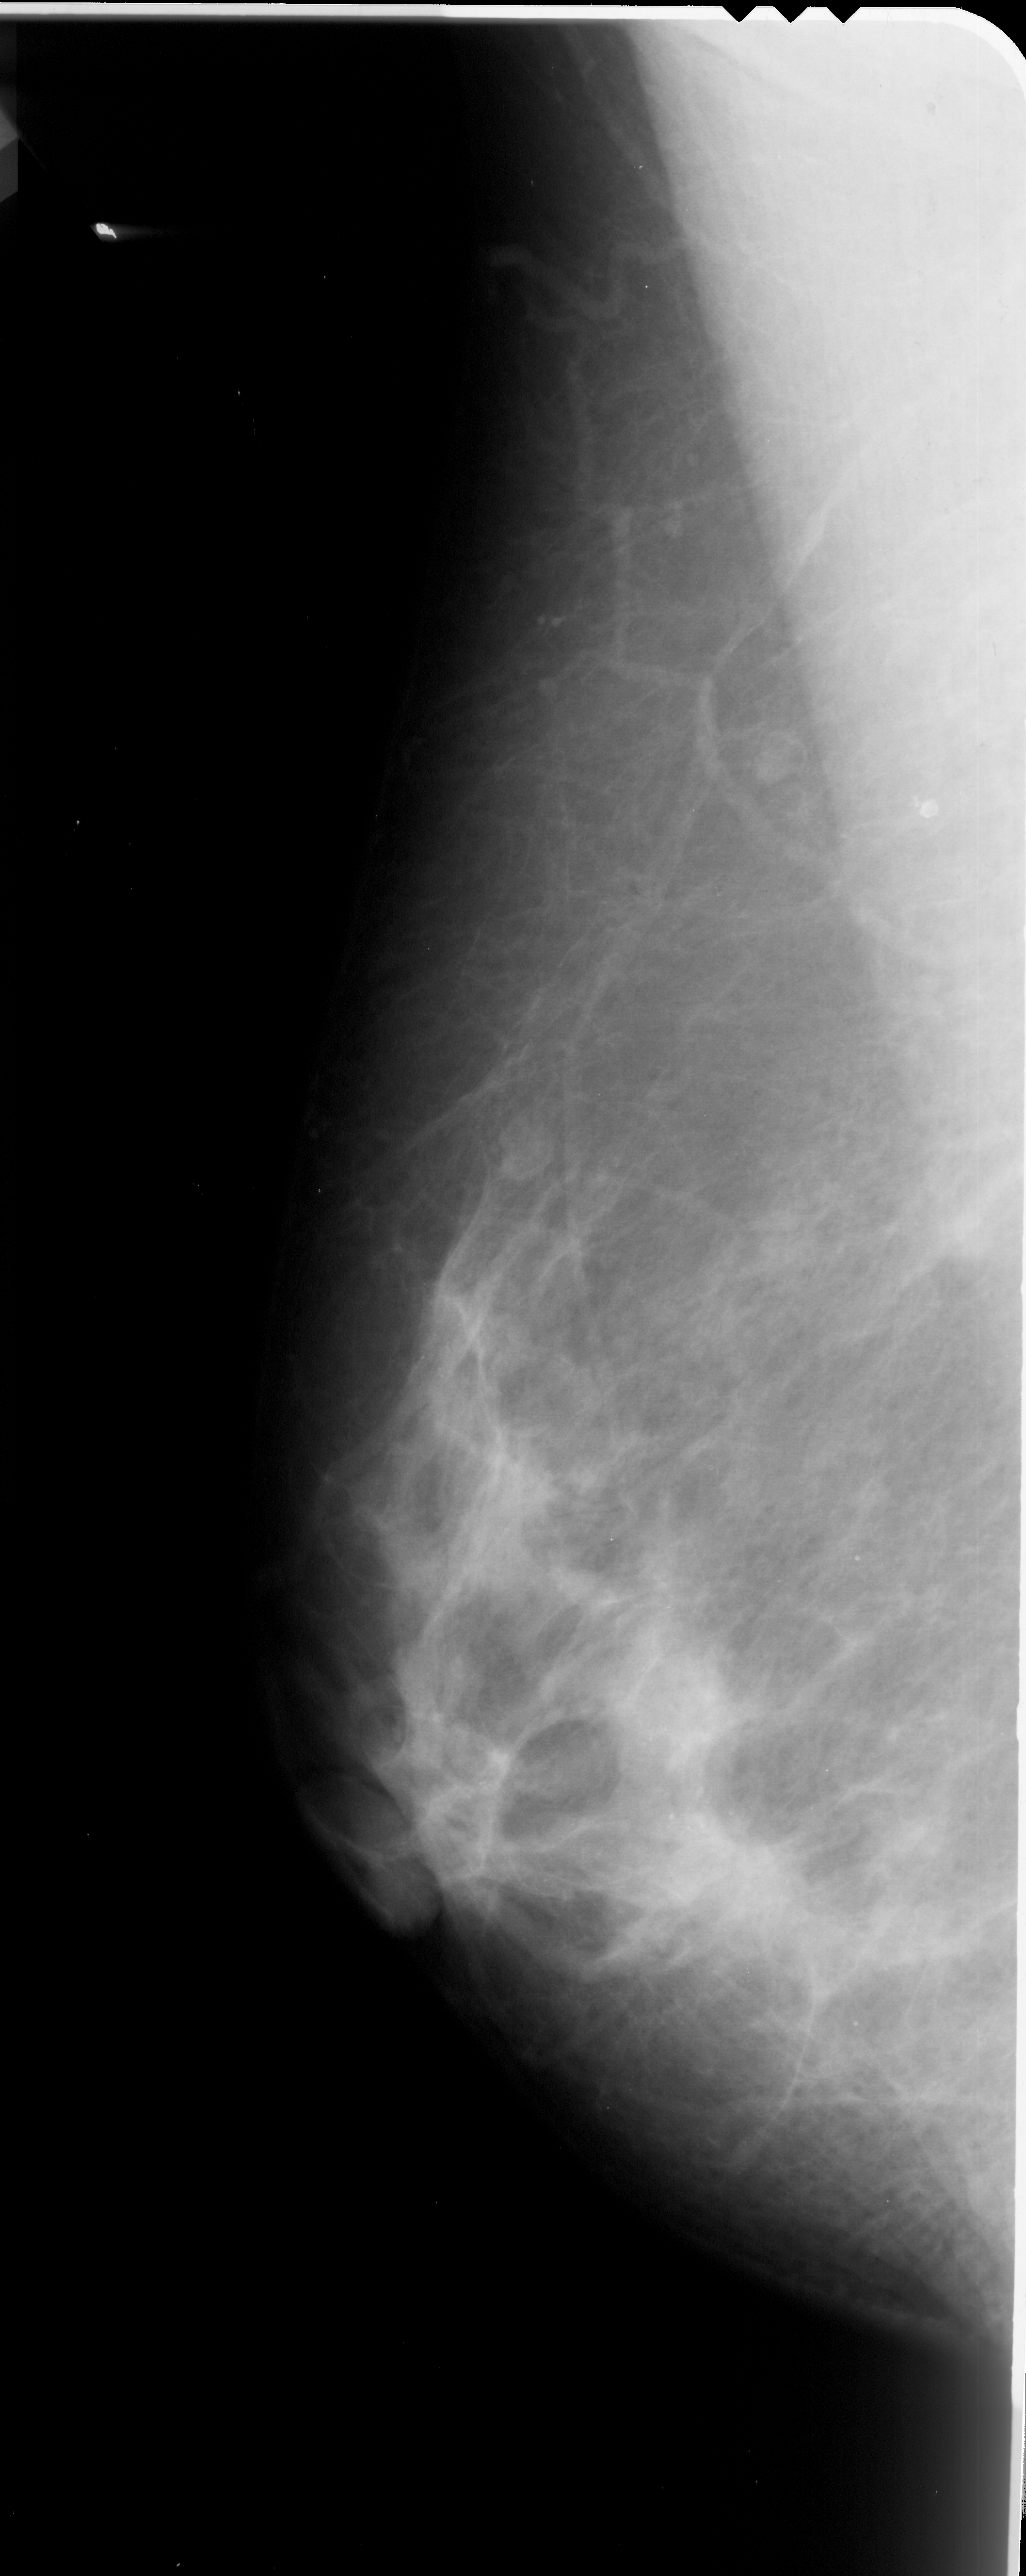
Mammogram (digitized film); left breast; MLO view; BI-RADS breast density category 3 (scale 1–4).
Calcifications, morphology pleomorphic, distribution clustered; BI-RADS assessment category 4; pathology (as recorded): malignant.